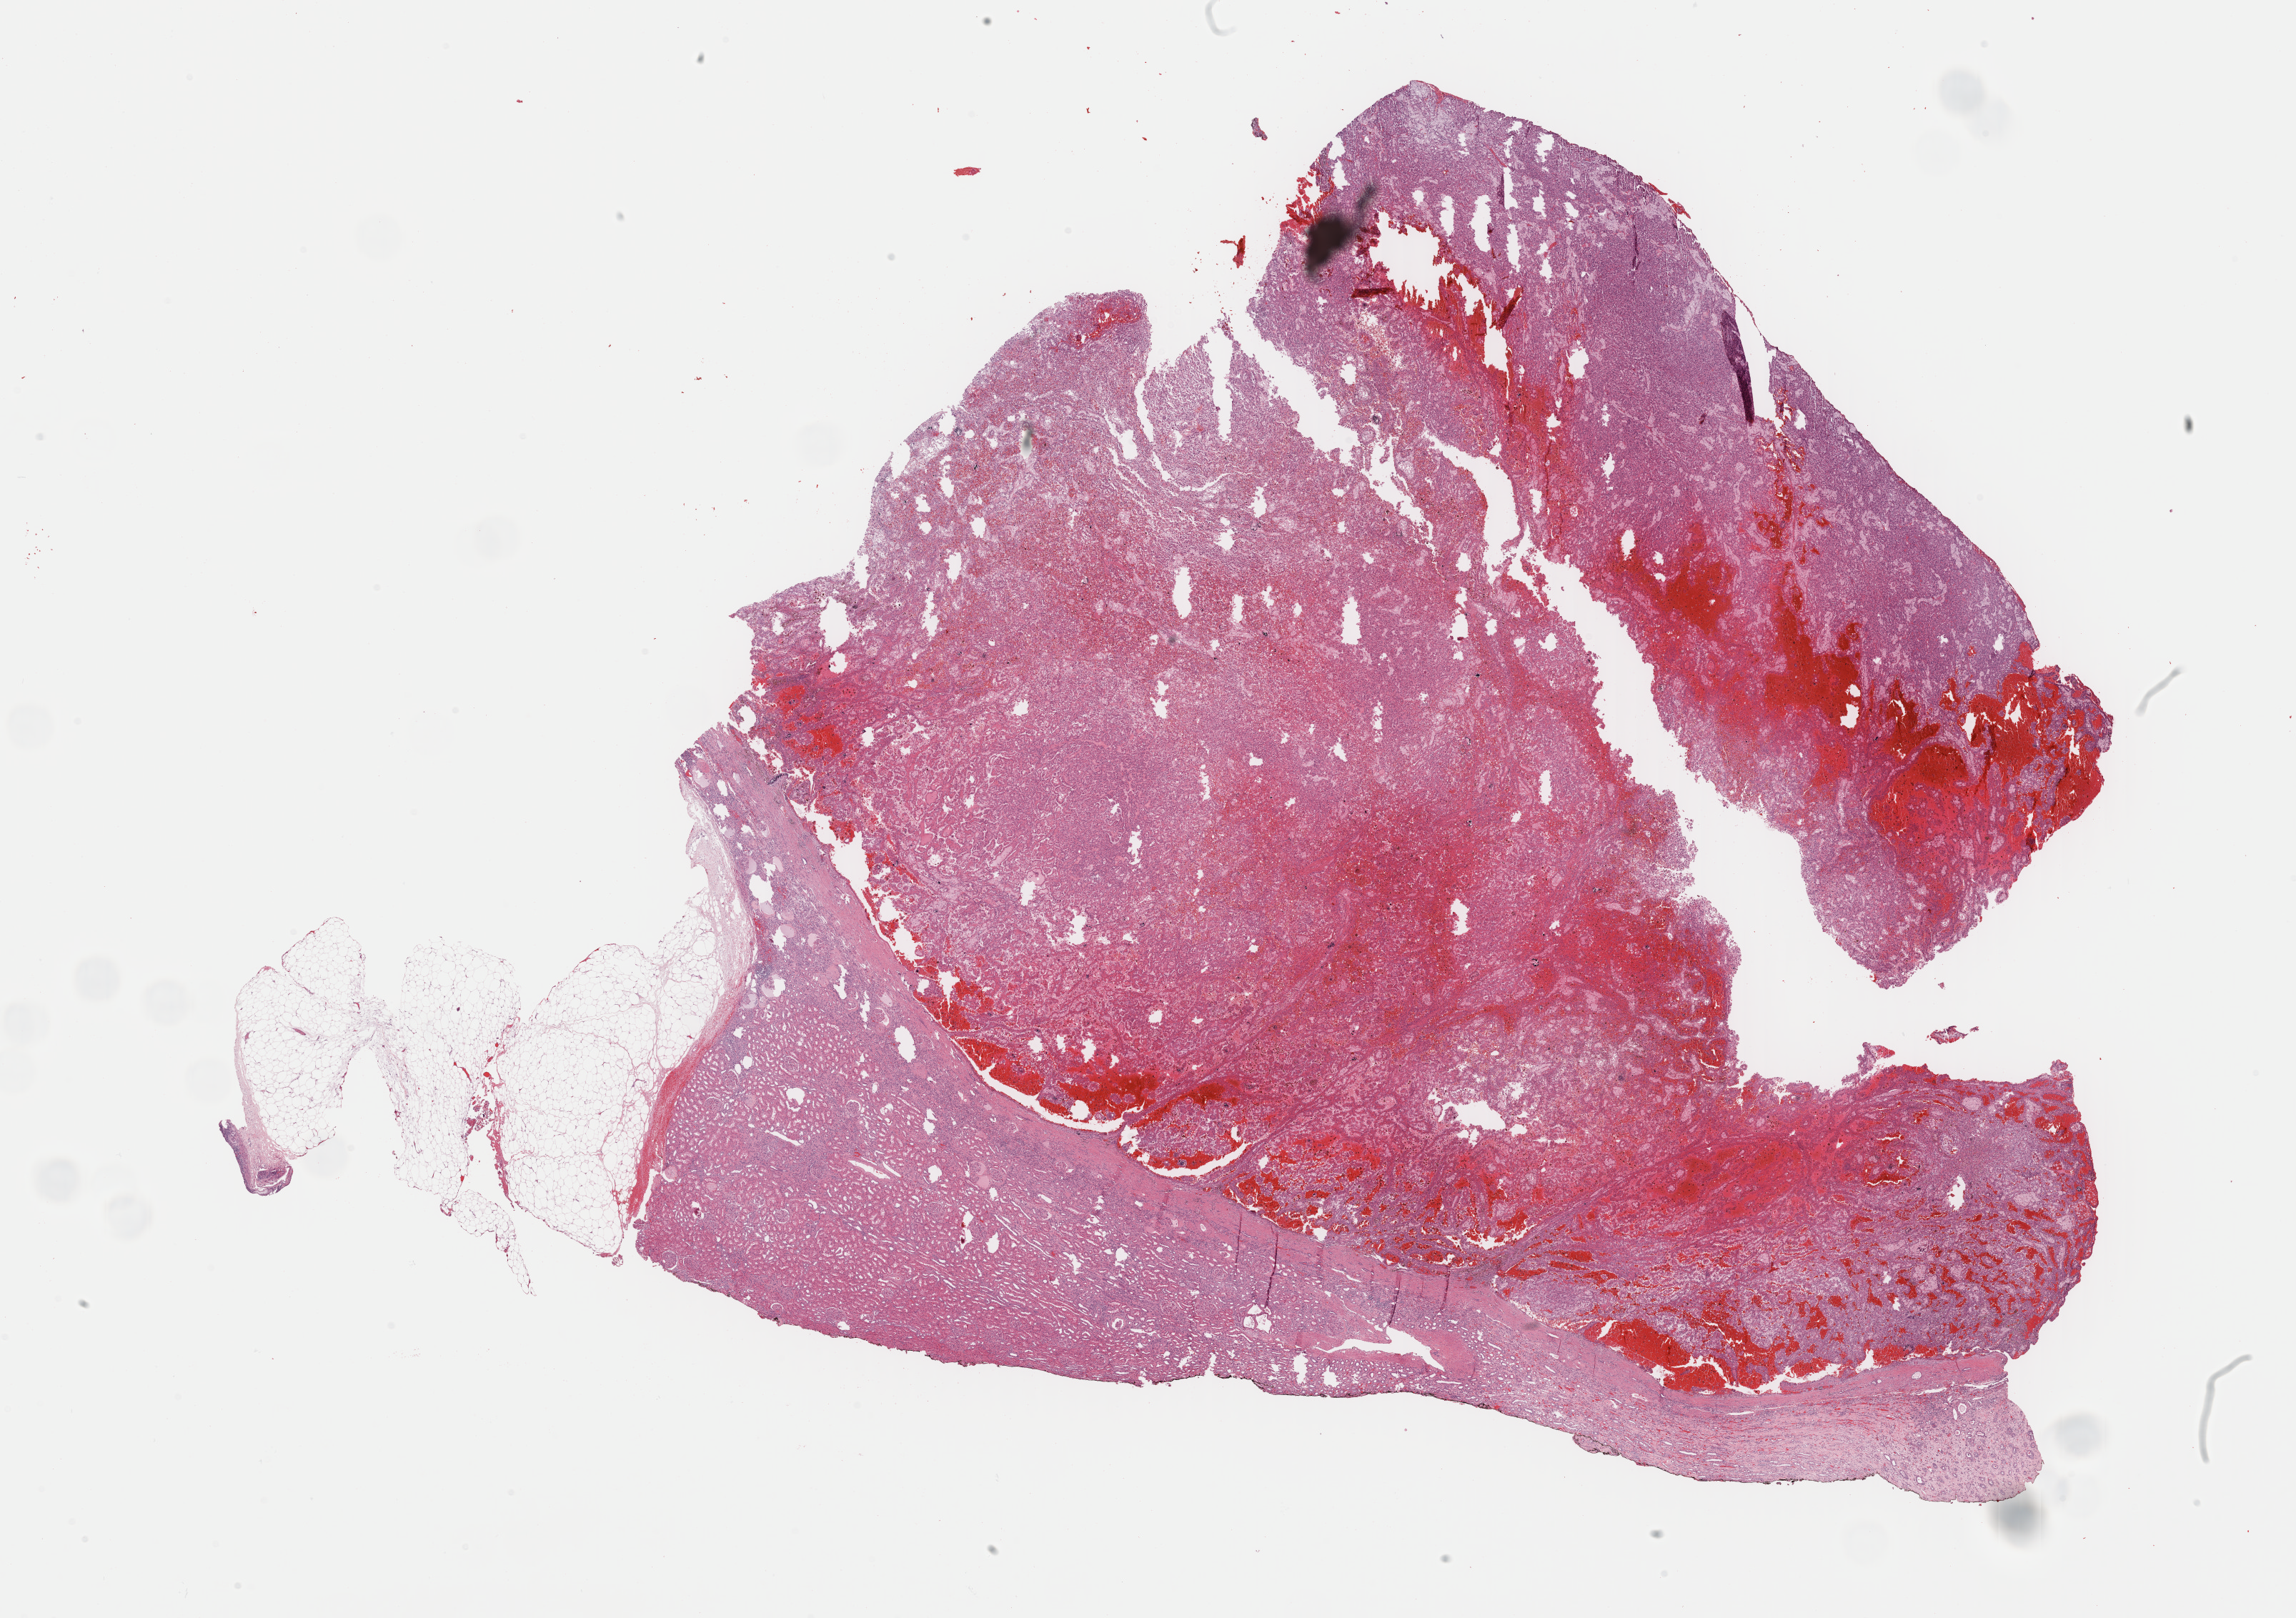
Whole-slide histology image, H&E, low-resolution overview of the scanned area, about 25.3 x 17.9 mm, FFPE section, kidney, primary tumour sample. Female patient; age at initial diagnosis 54 years.
Laterality: right. AJCC pathologic stage: I. Diagnosis: Papillary adenocarcinoma, NOS.